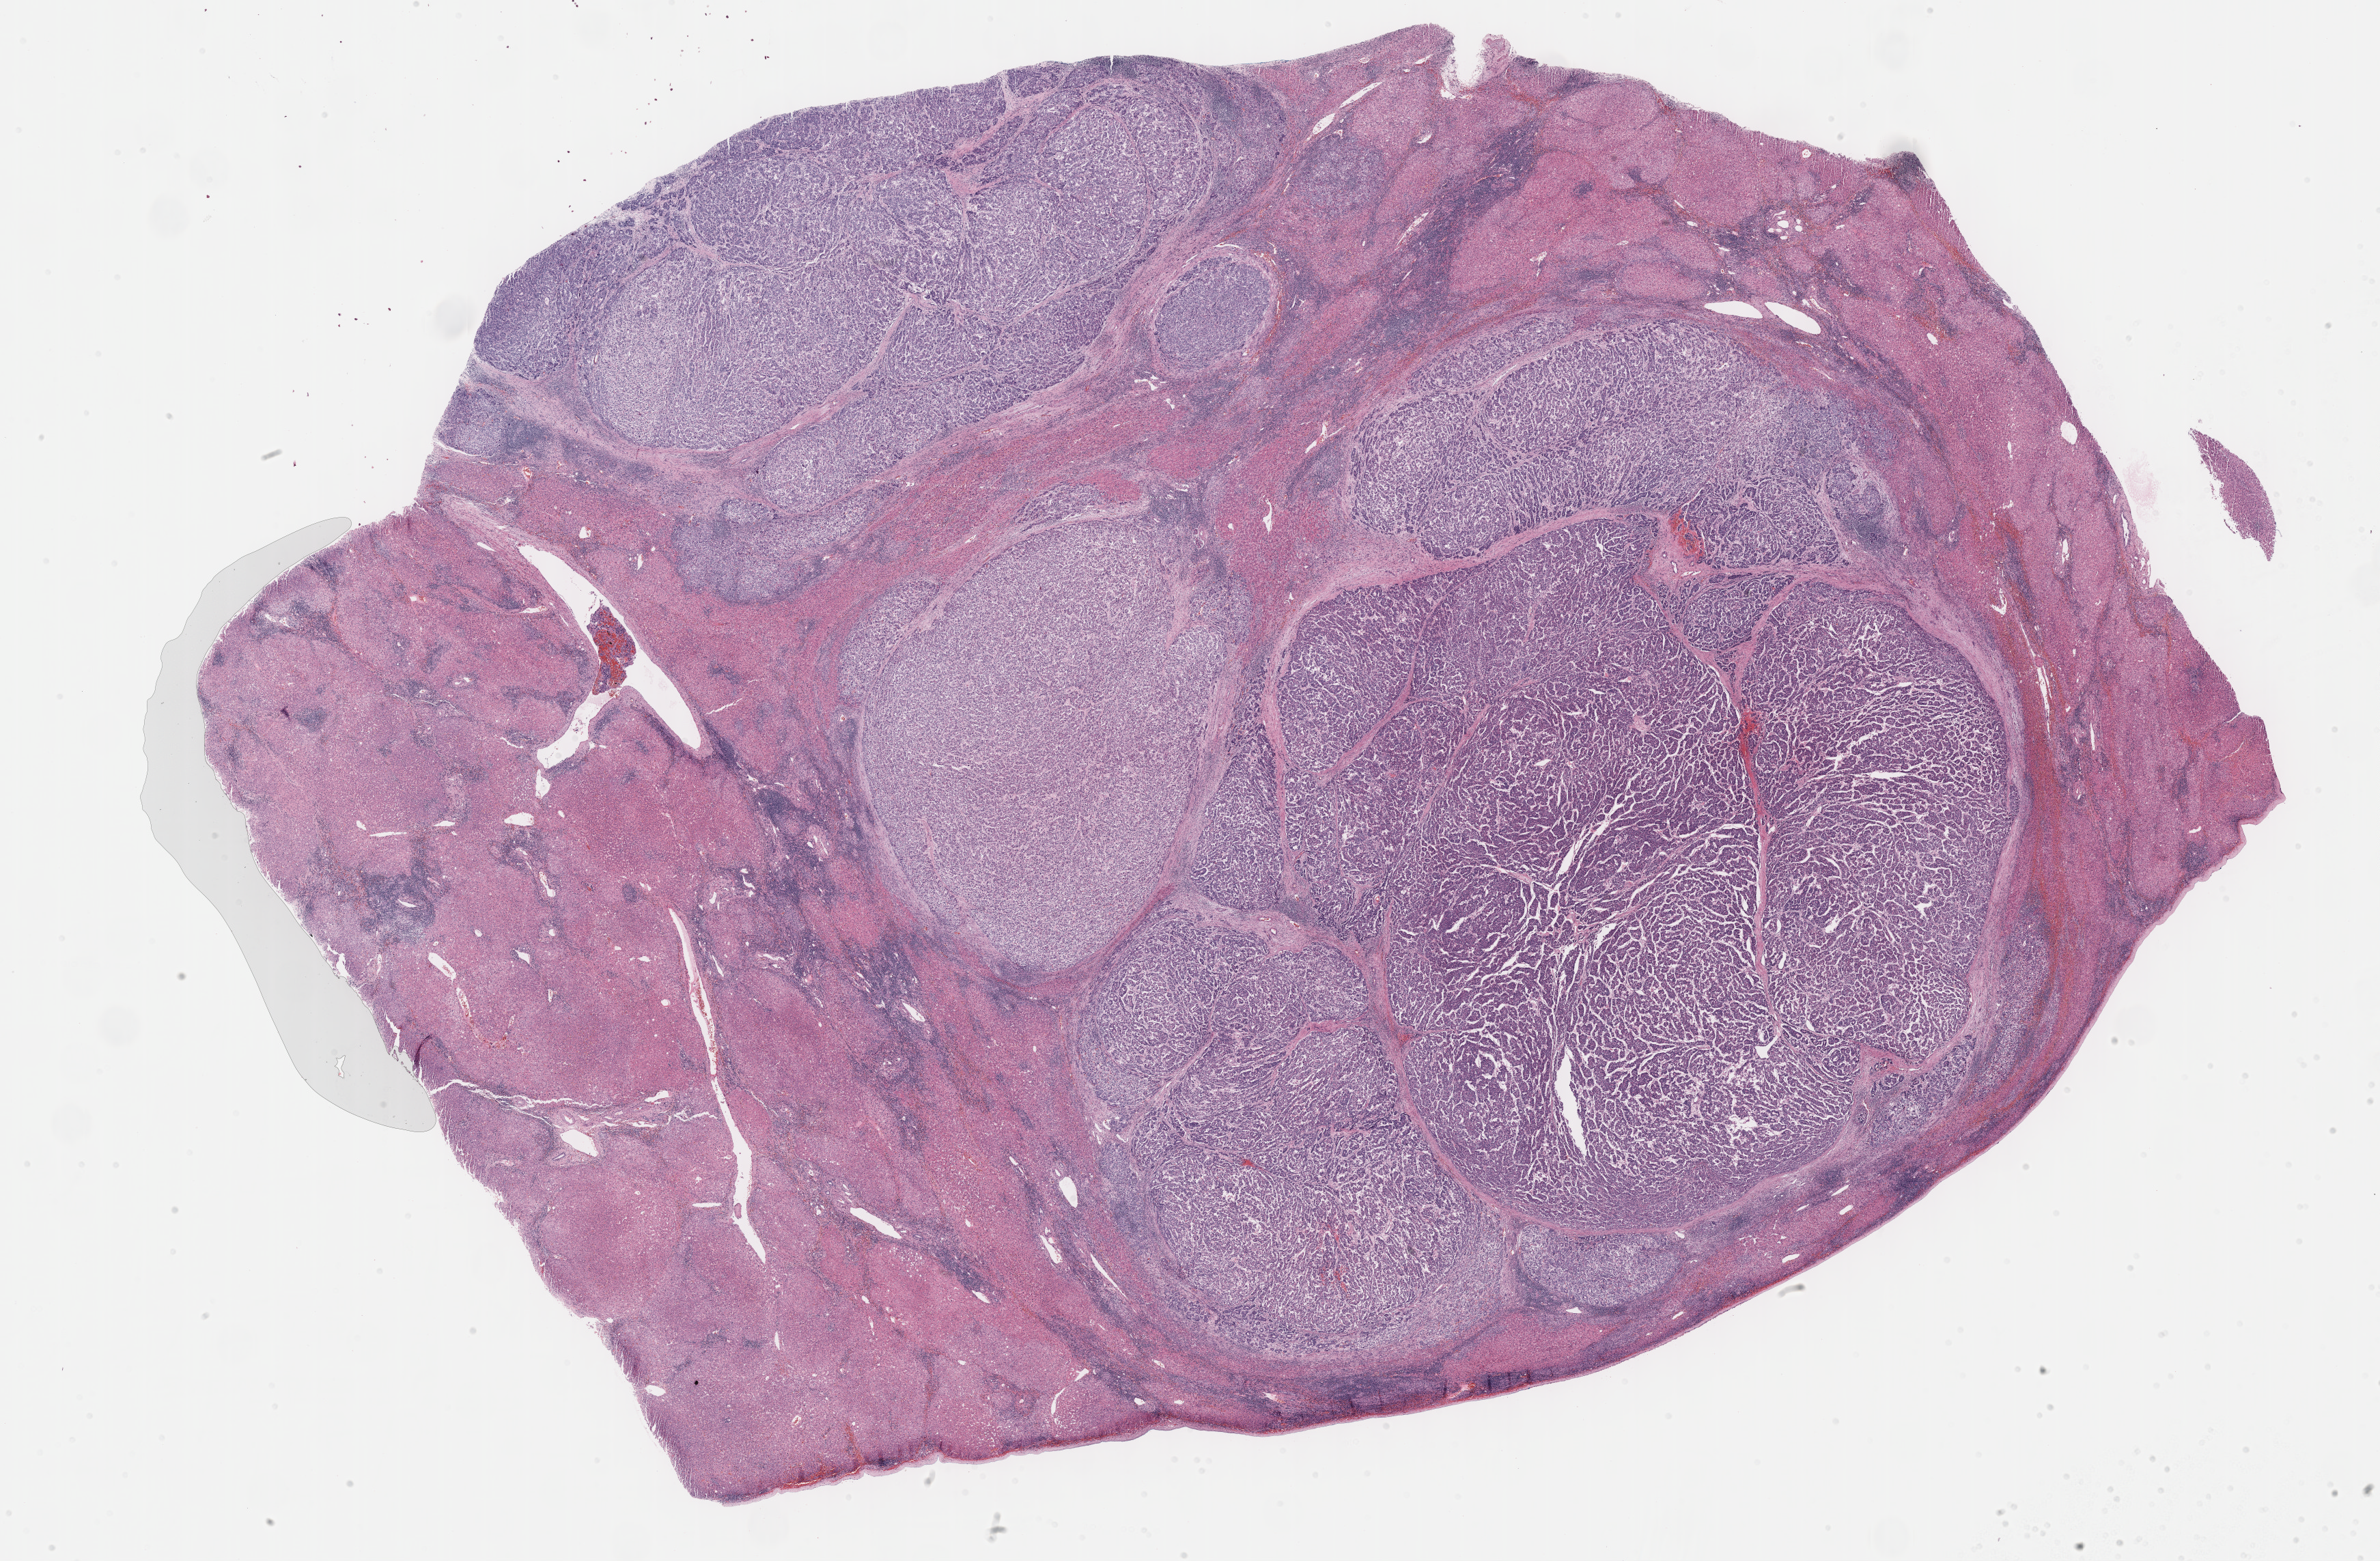
Digitized H&E tissue section (whole slide), low-resolution overview of the scanned area, about 28.2 x 18.5 mm (from a 40x scan), FFPE section, primary tumour sample from the liver. Female, age 64 years at initial diagnosis. Histologic grade: G3 (poorly differentiated).
* AJCC pathologic stage: I (7th edition)
* histologic diagnosis: Hepatocellular carcinoma, NOS